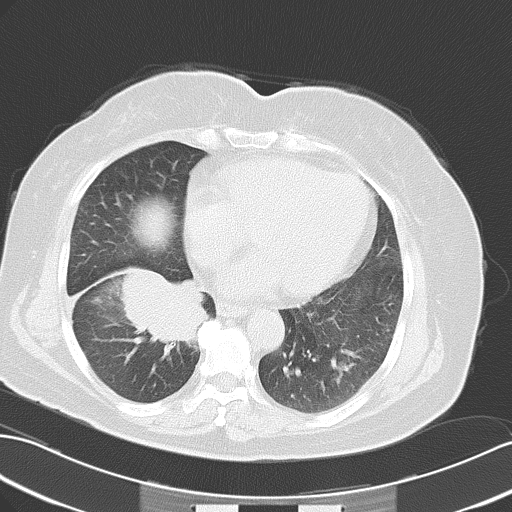
Chest CT, one axial slice; position 20 of 50 along the scan axis; reconstruction kernel B70f; 120 kVp; lung window (W 1500 / L -600 HU); 5 mm slice thickness; 512 × 512 image matrix, field of view 353 × 353 mm. Female patient, age 63 years. From the clinical record (not read from this slice): clinical TNM (as recorded): T3 N0 M0.
Structures marked on this image (rectangle marked by the reading radiologist):
- lung tumour (recorded histology: adenocarcinoma): box from (x=113, y=268) to (x=207, y=348) px